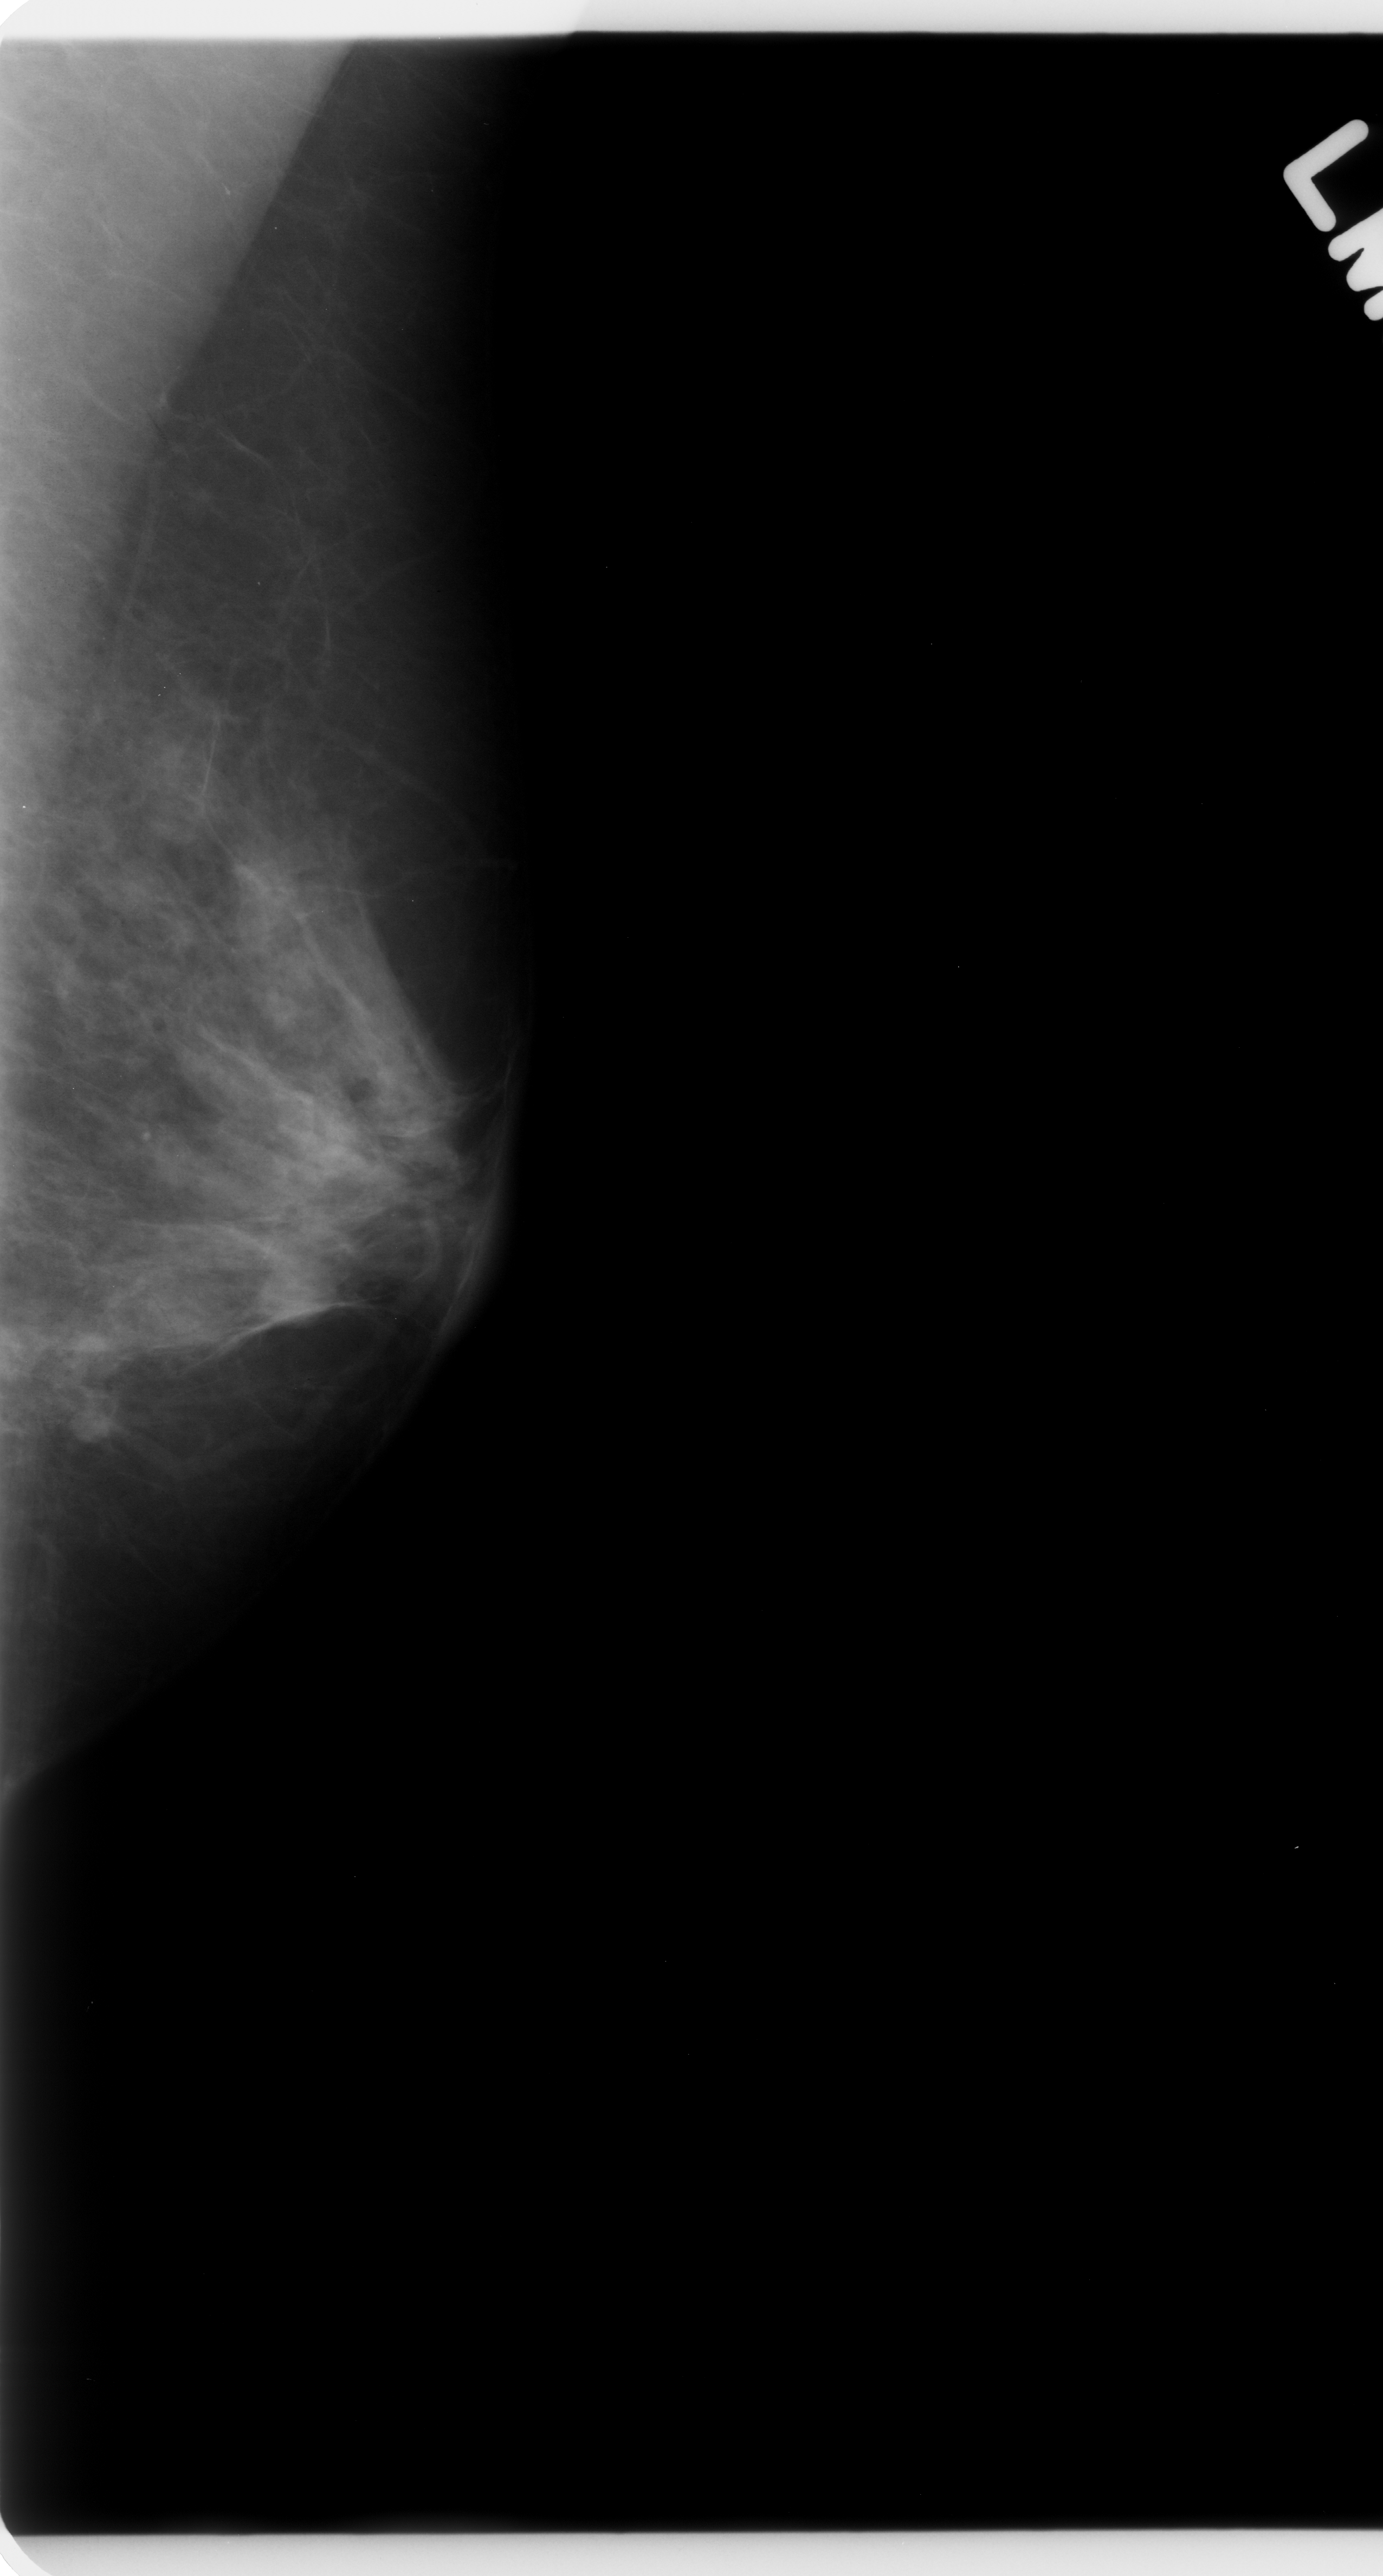
Scanned film-screen mammogram, left breast, MLO view, BI-RADS breast density category 3 (scale 1–4).
Mass, shape oval, margins circumscribed; BI-RADS assessment category 4; subtlety rating 4 on a 1 (subtle) to 5 (obvious) scale; pathology (as recorded): benign.